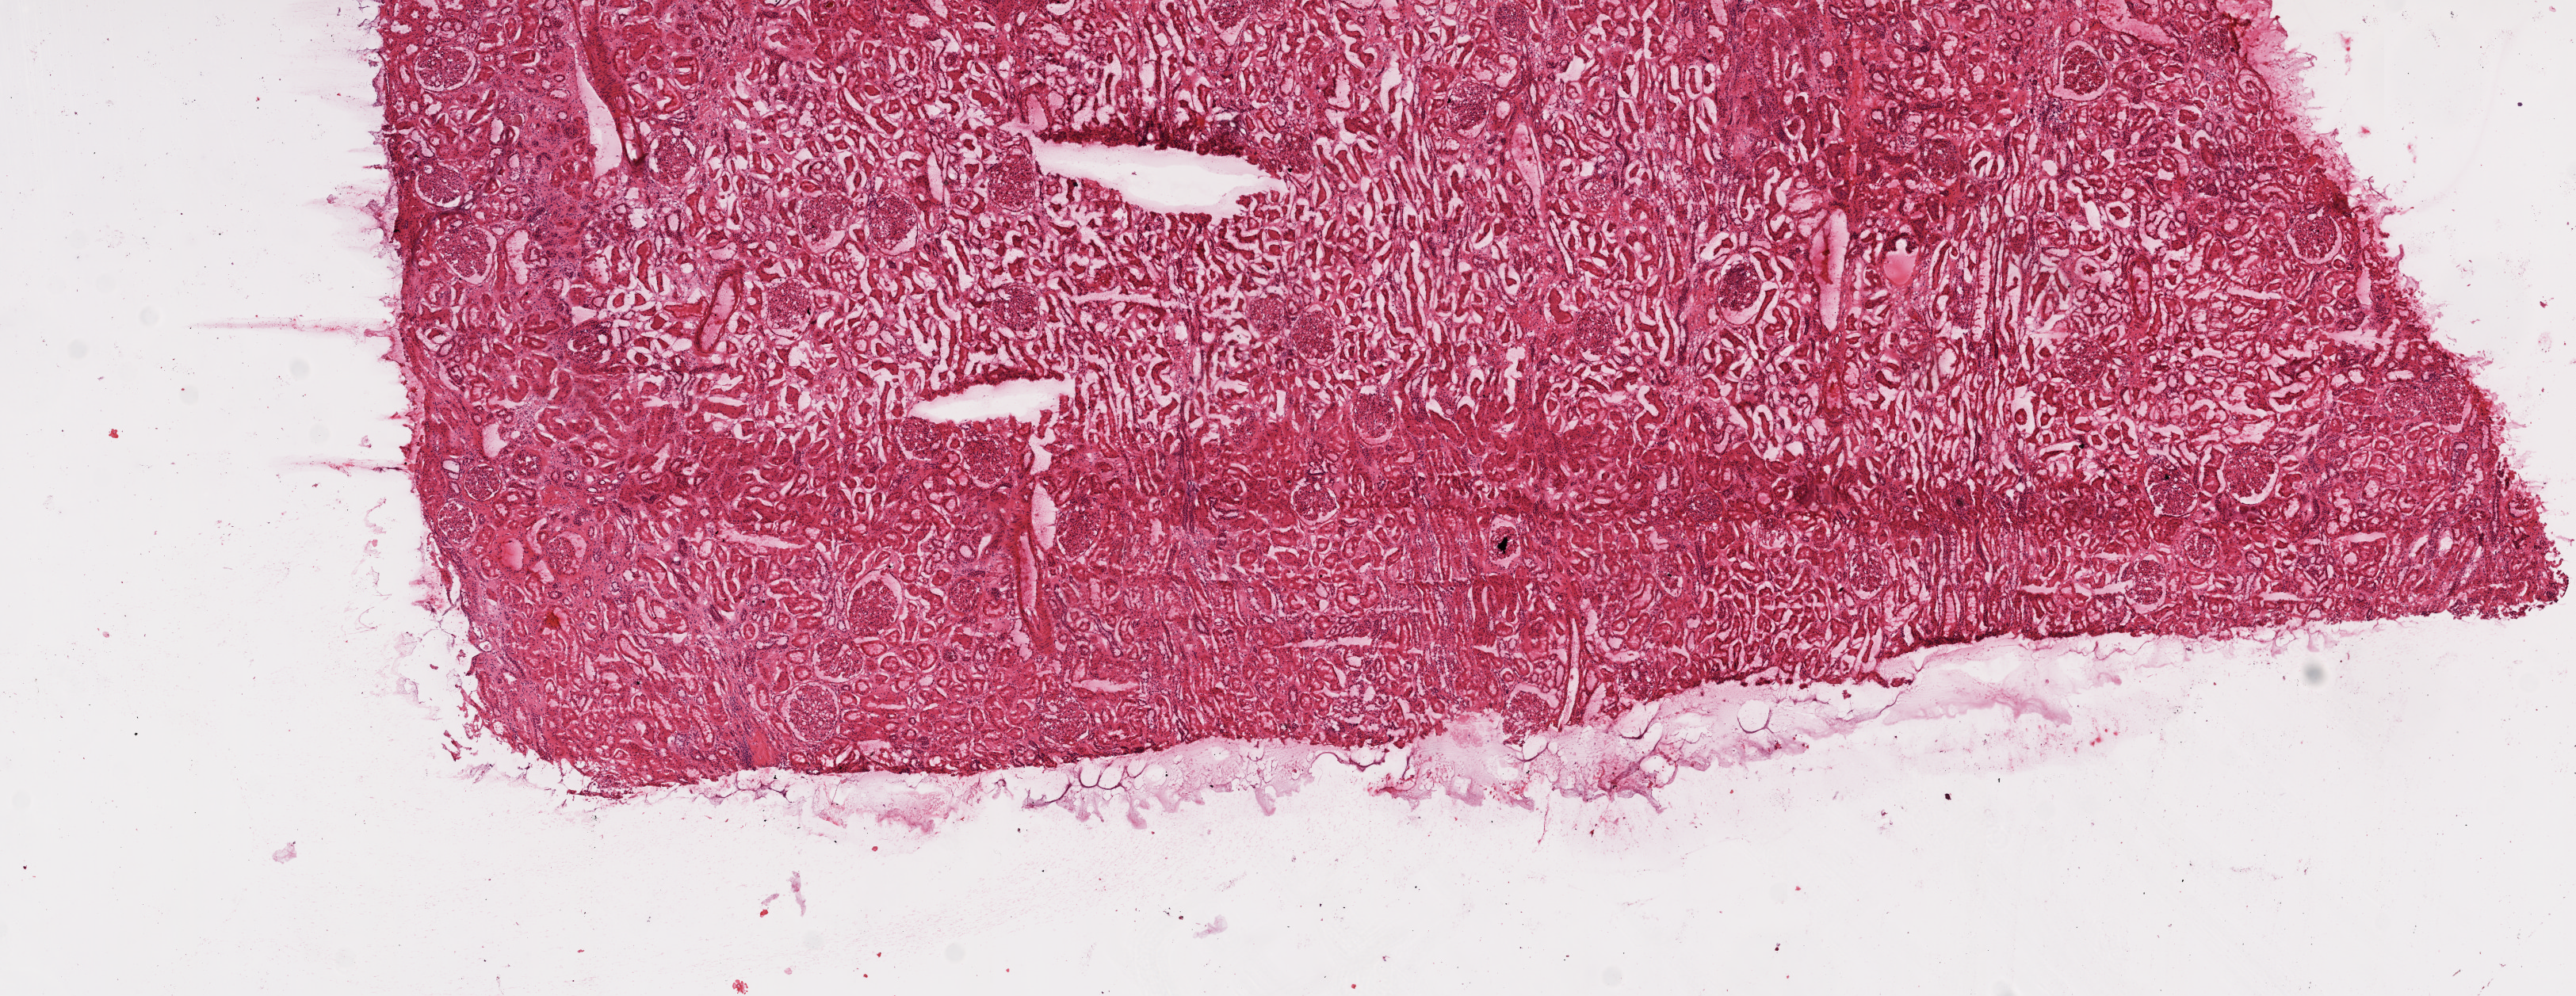
Whole-slide histology image, H&E, low-resolution overview of the scanned area, about 13.0 x 5.0 mm. Frozen section from the top of the tissue portion. Sample: solid tissue normal (non-tumour tissue), kidney. Patient: male, age at initial diagnosis 64 years.
This section: solid tissue normal (non-tumour) sample from the same patient. Patient diagnosis: Clear cell adenocarcinoma, NOS.